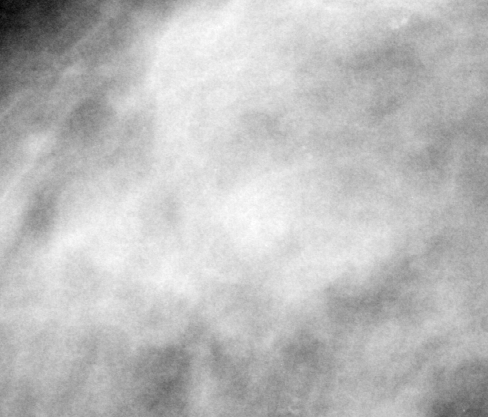
Crop from a digitized film mammogram around one marked abnormality; right breast; MLO view.
Mass, shape irregular, margins ill defined; BI-RADS assessment category 4; subtlety rating 3 on a 1 (subtle) to 5 (obvious) scale; pathology (as recorded): malignant.